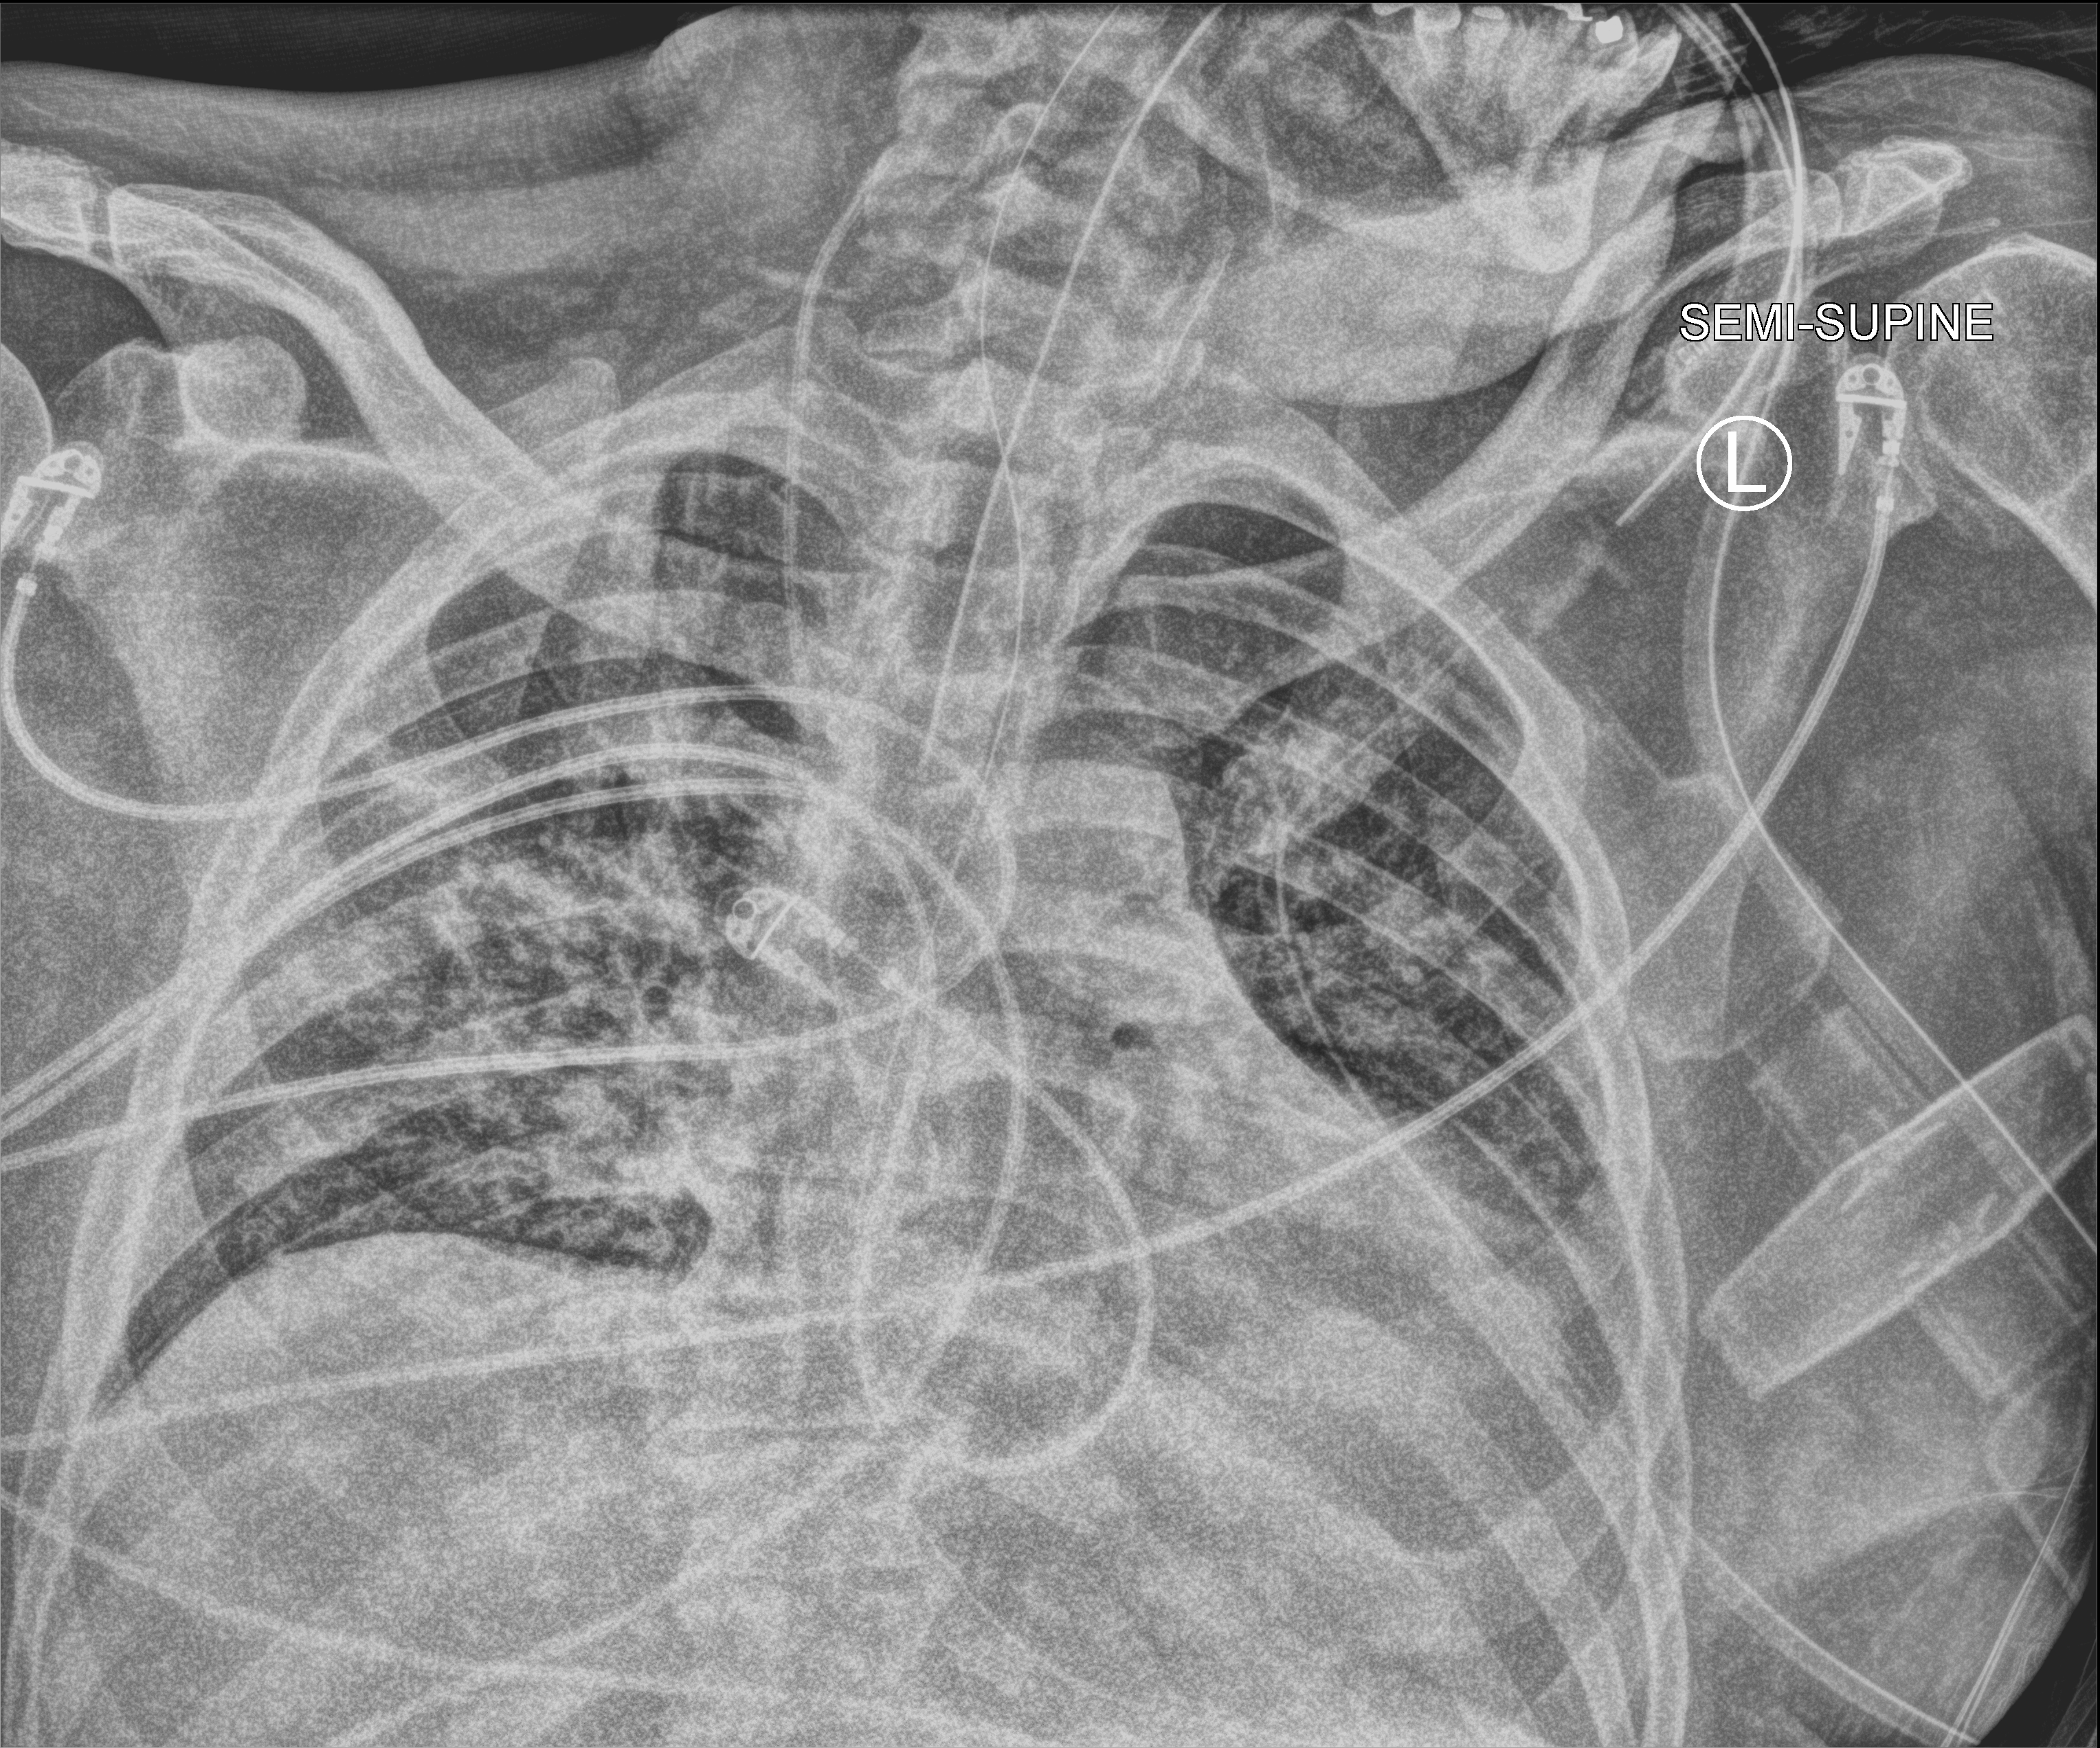
Portable chest radiograph; anteroposterior (AP) projection. Male patient hospitalised with COVID-19, age 18–59 years.
Hospital-stay facts (about this admission, not read from this image; timing relative to this image not recorded): admitted to intensive care during this hospital stay: yes; mechanically ventilated during this hospital stay: yes.